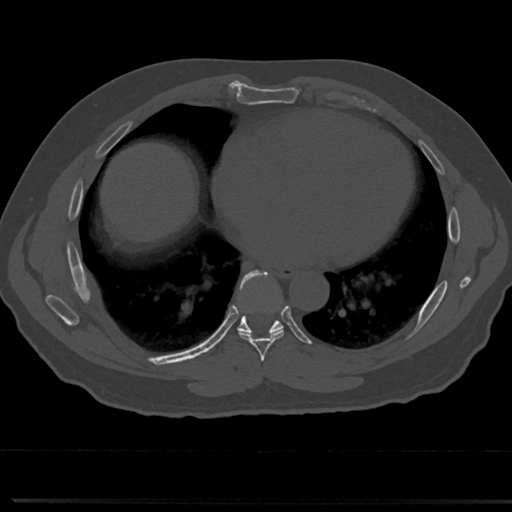
CT including the spine, one axial slice; slice 384 of 817 in the series (ordered by position); reconstruction kernel Br40s/3; 120 kVp; bone window (W 1800 / L 400 HU); 512 × 512 image matrix, field of view 355 × 355 mm. Male patient, age 61 years. From the clinical record (not read from this slice): primary cancer: prostate.
Outlined on this slice (semi-automatically segmented with operator editing):
- T6 vertebra: box from (x=260, y=367) to (x=268, y=377) px
- T7 vertebra: (x=228, y=273)–(x=308, y=353)